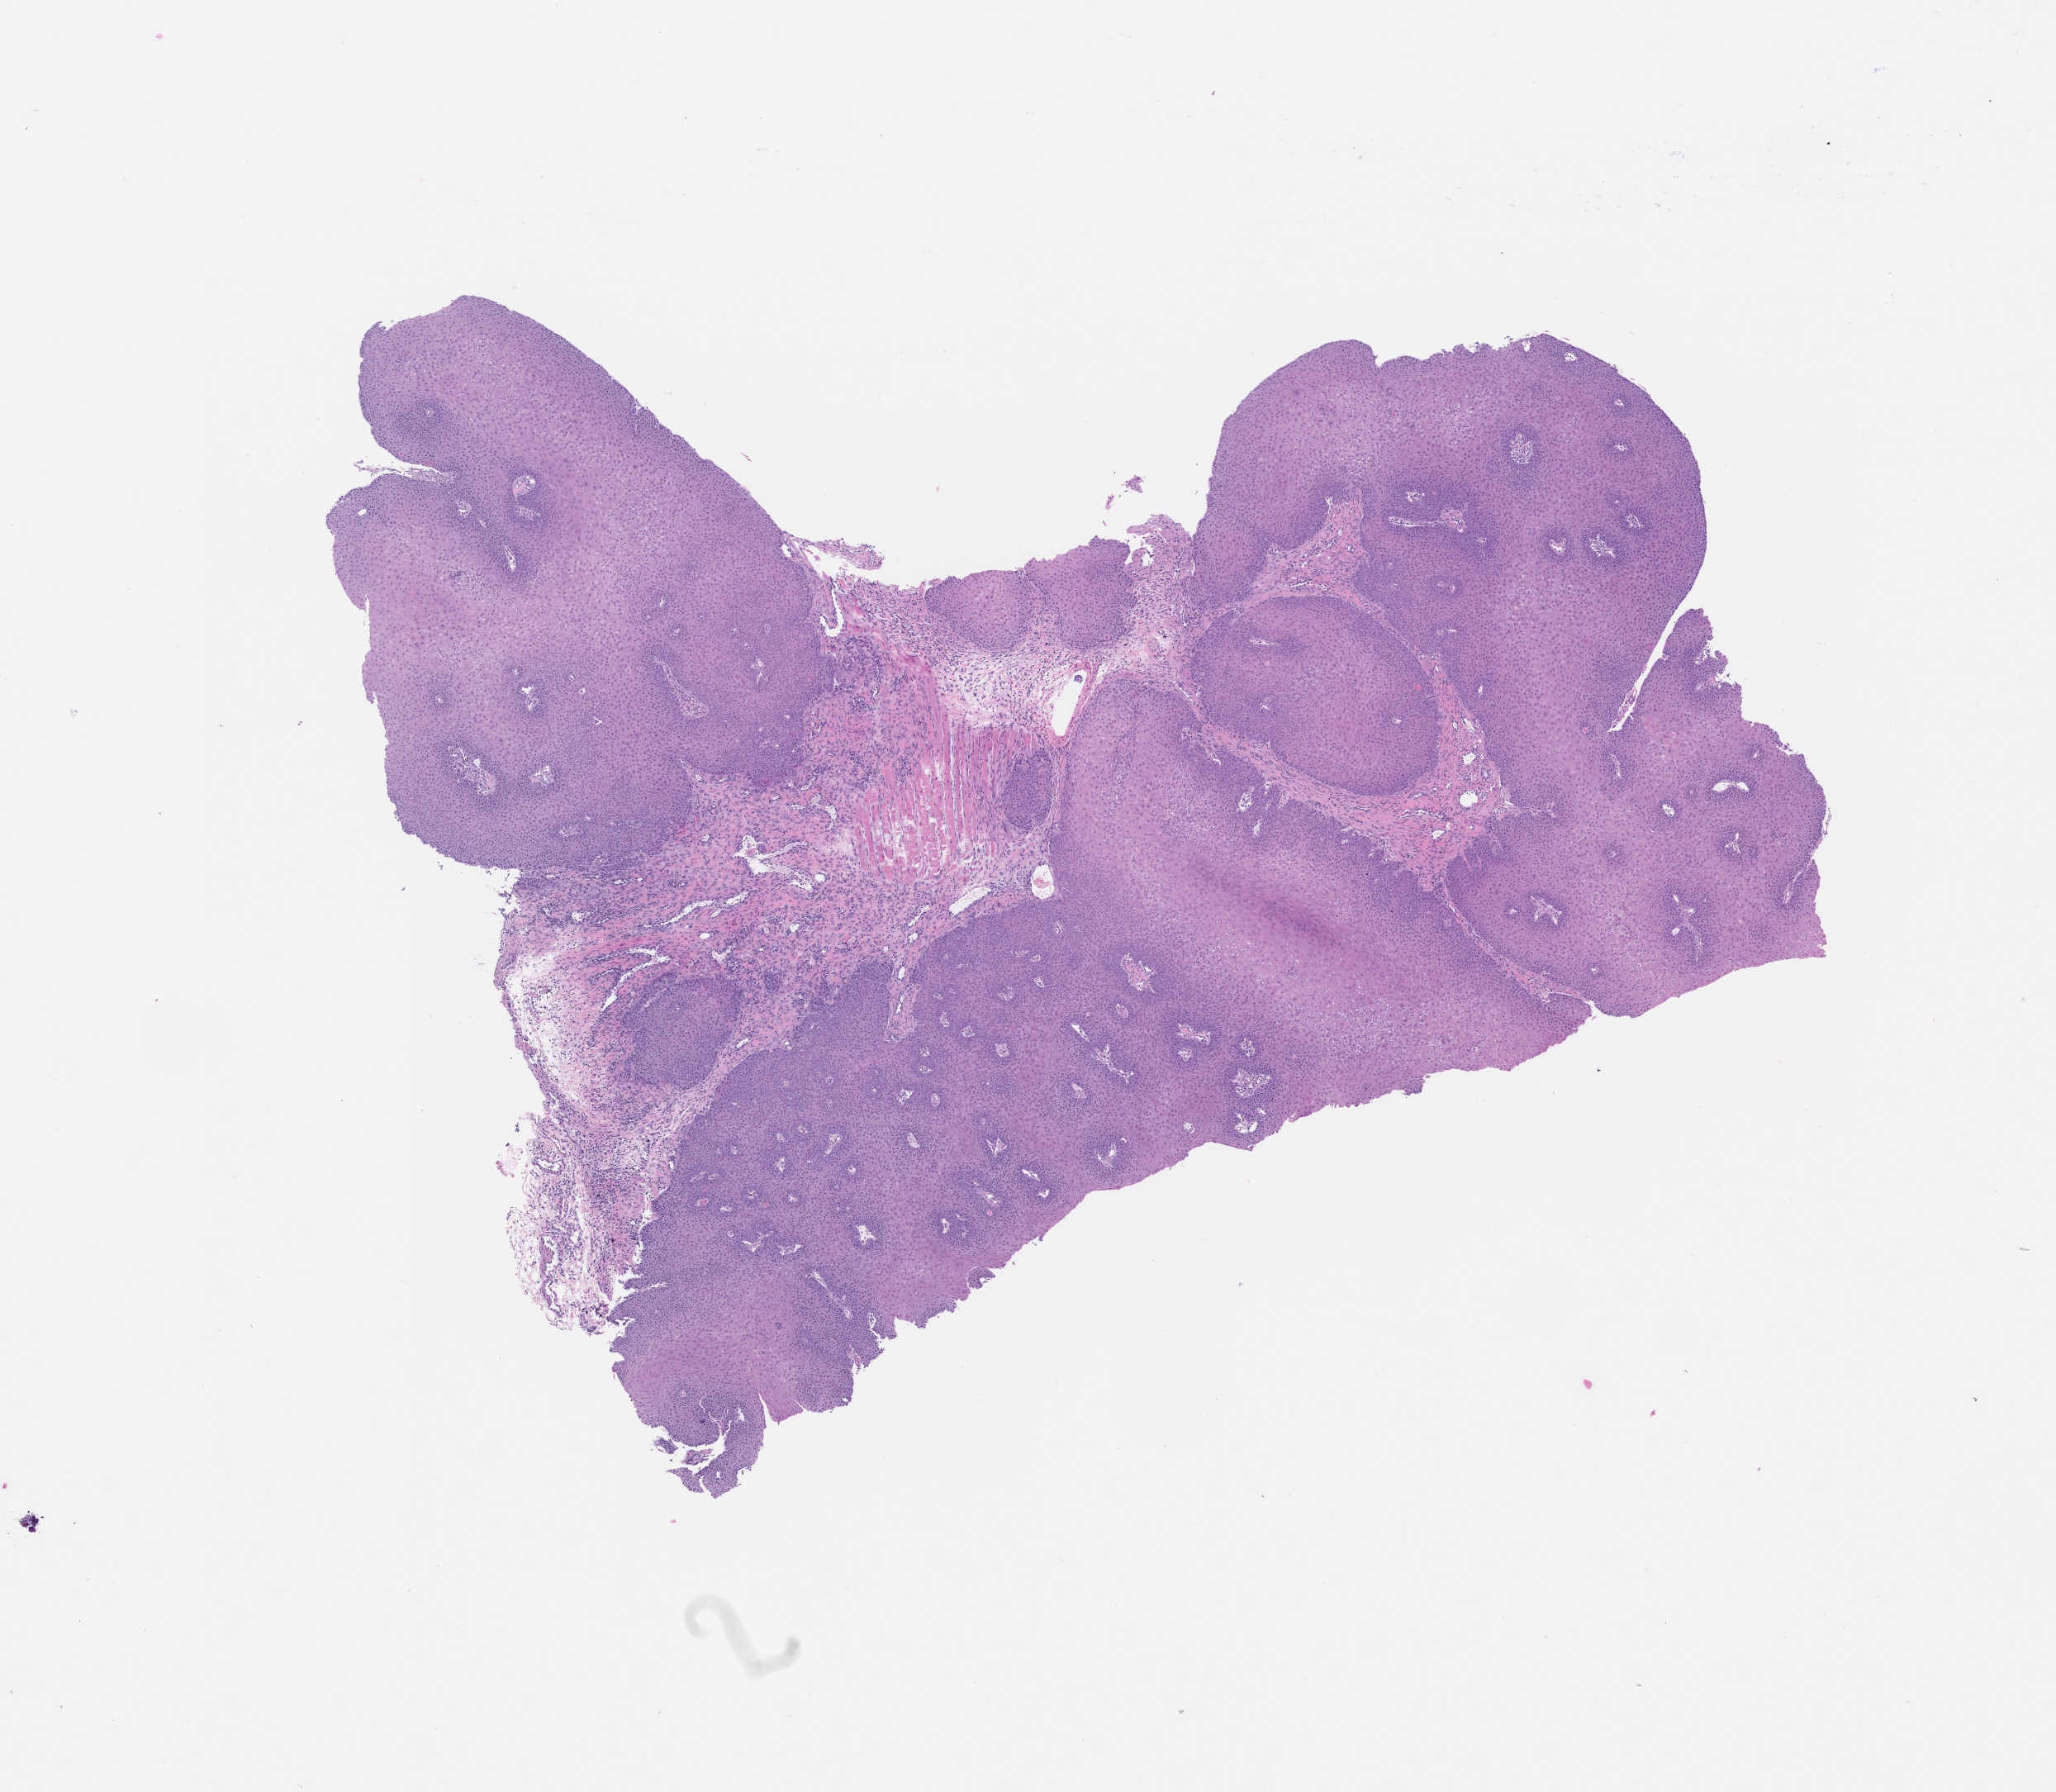
Whole-slide image, hematoxylin and eosin (H&E): patient-derived xenograft (human tumor grown in a mouse), passage 1, a low-resolution overview of the entire scanned area, about 10.0 x 8.7 mm; formalin-fixed paraffin-embedded section; tumor site category: bladder.
Originating patient diagnosis: Transitional Cell Carcinoma.